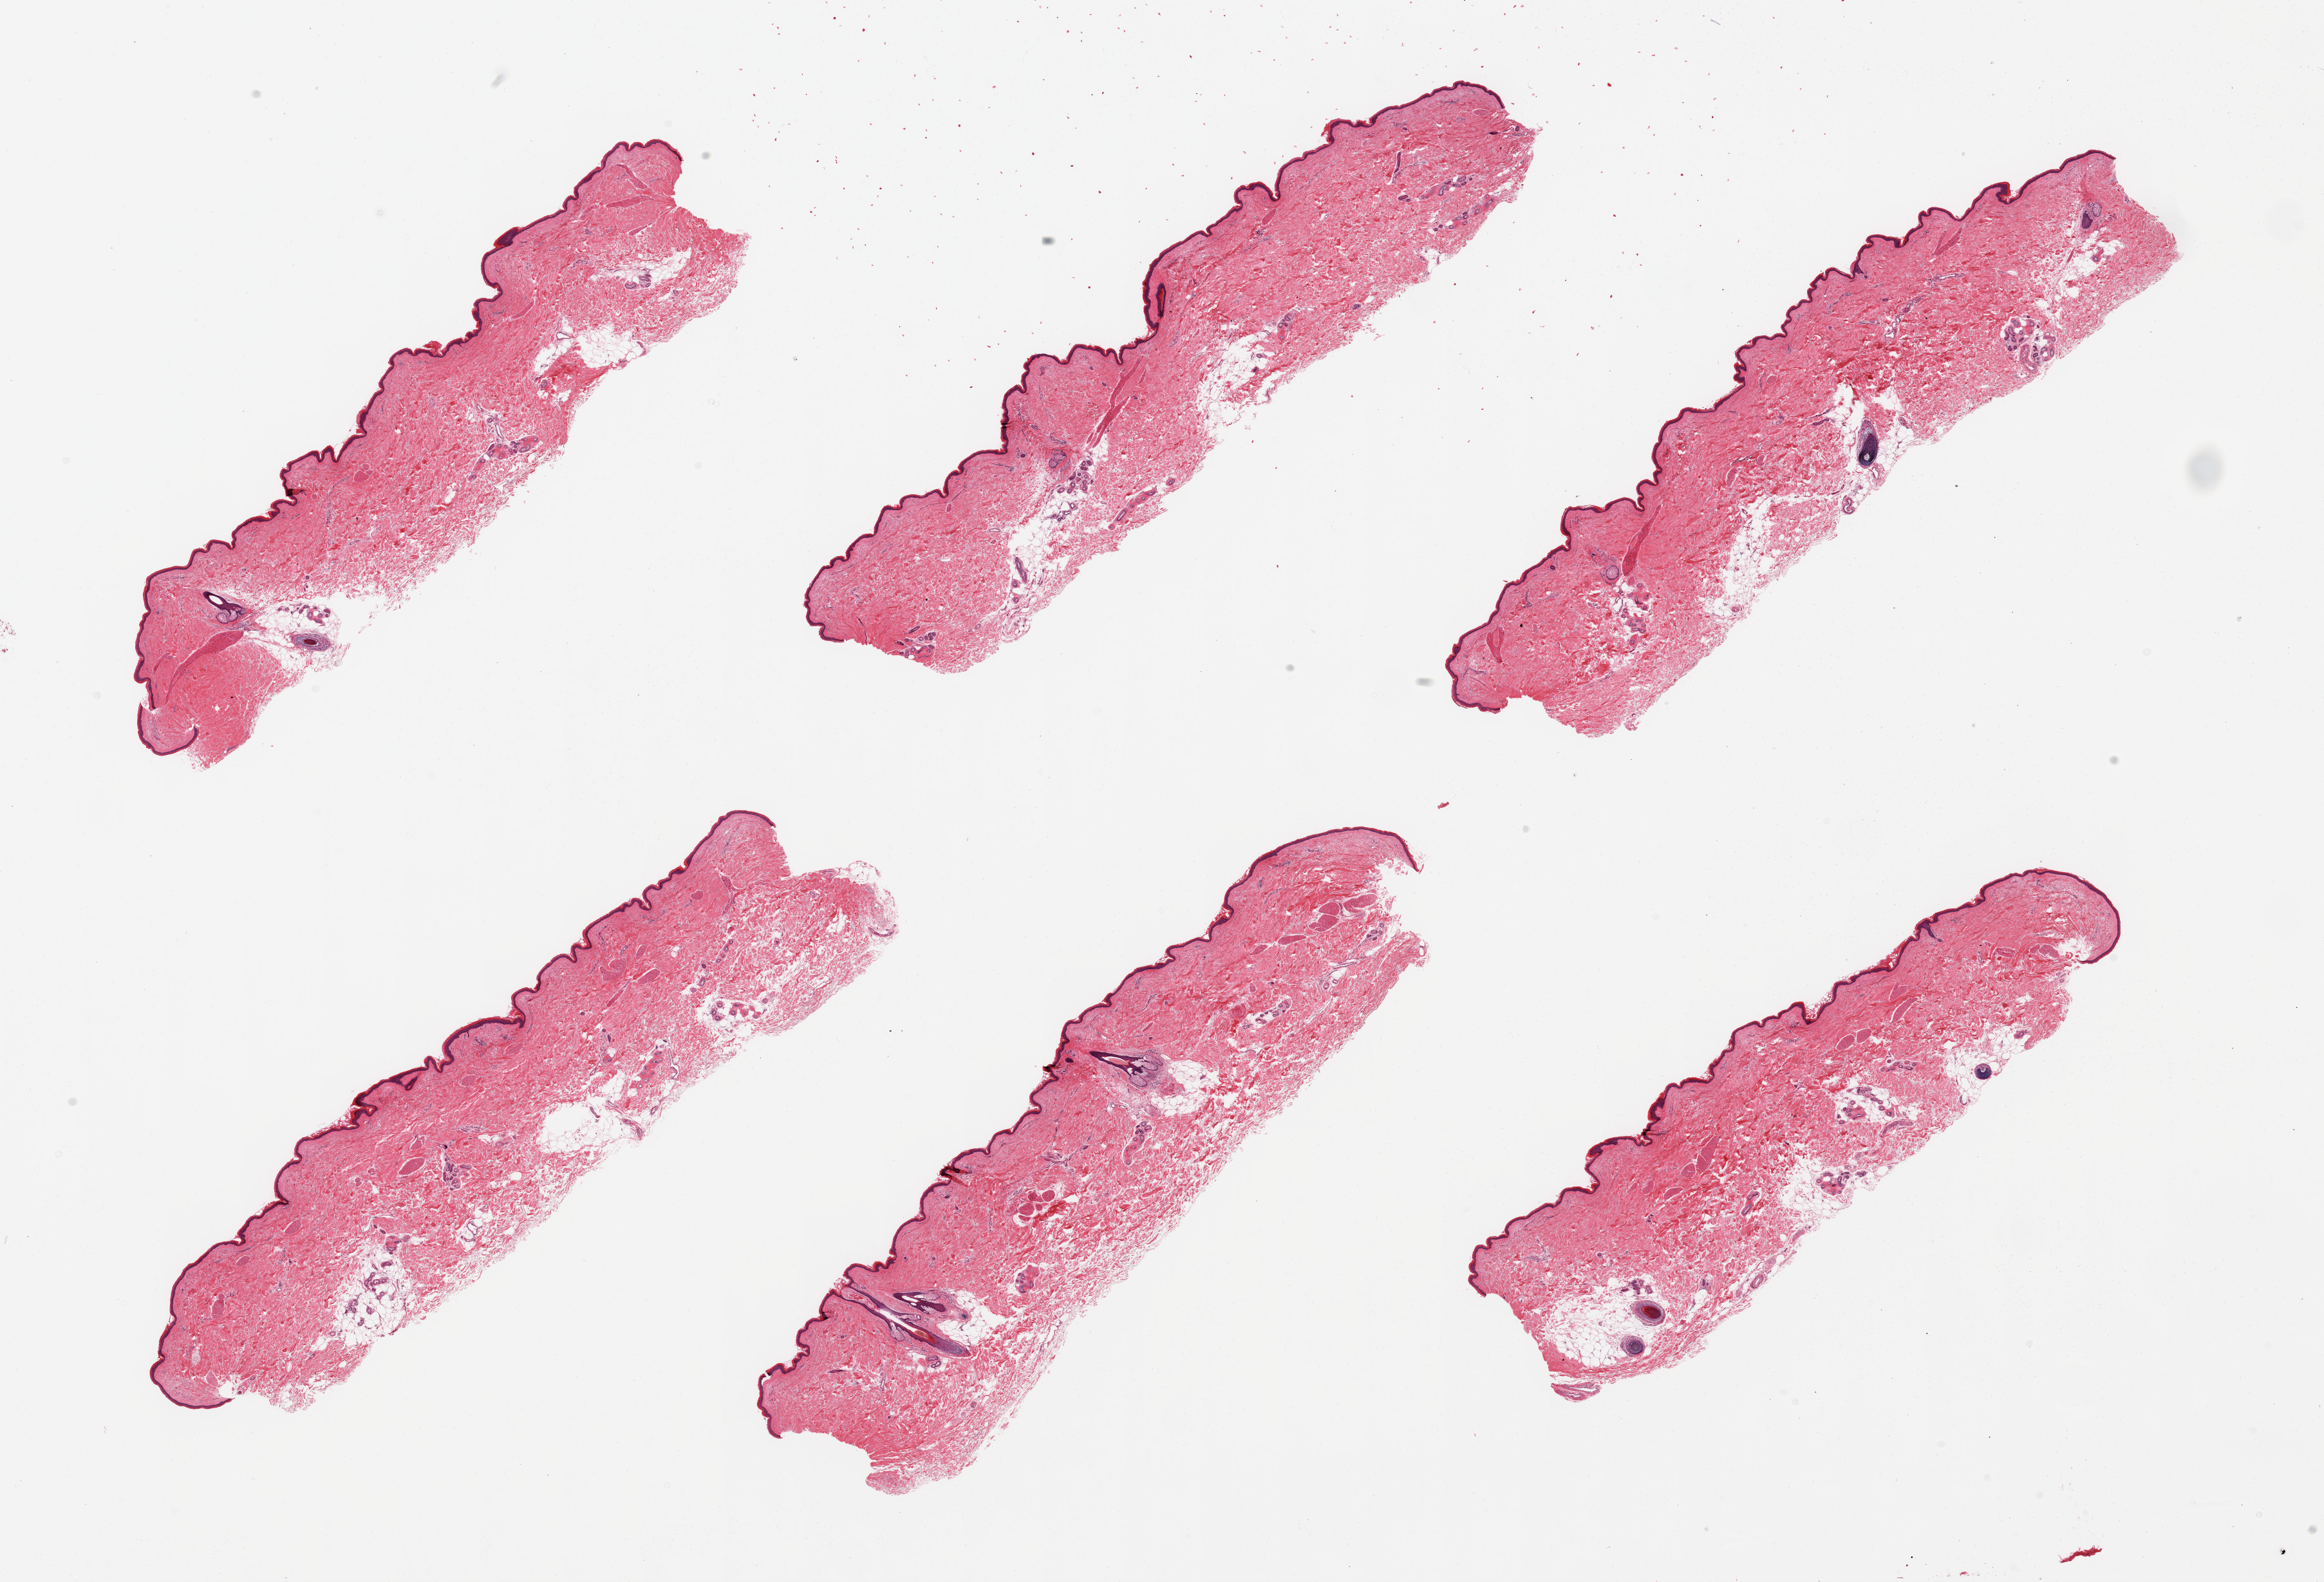
Digitized hematoxylin and eosin (H&E)-stained section, a low-resolution overview of the entire scanned area, about 28.5 x 19.4 mm (slide scanned at 20x), PAXgene-fixed paraffin-embedded (PFPE) section, section of skin of lower leg (target tissue), donor tissue sample. Male donor.
Pathologist's review note for this sample: 6 pieces; well trimmed; 10% intradermal fat.